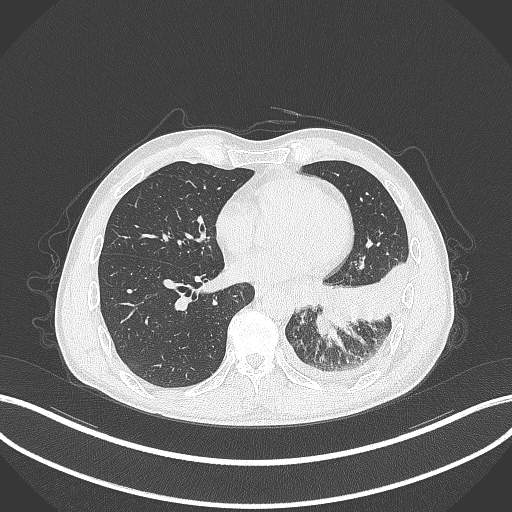
Chest CT, one axial slice. Position 118 of 295 along the scan axis. Reconstruction kernel B70f. 120 kVp. Lung window (W 1500 / L -600 HU). 512 × 512 image matrix, field of view 400 × 400 mm. Male patient, age 47 years. Case-level facts recorded for this patient, not image findings: clinical TNM (as recorded): T3 N1 M1c.
Structures marked on this image (bounding box drawn by a radiologist):
- lung tumour (recorded histology: small cell carcinoma): bounding box (x1, y1, x2, y2) in pixels: (311, 304, 336, 338)